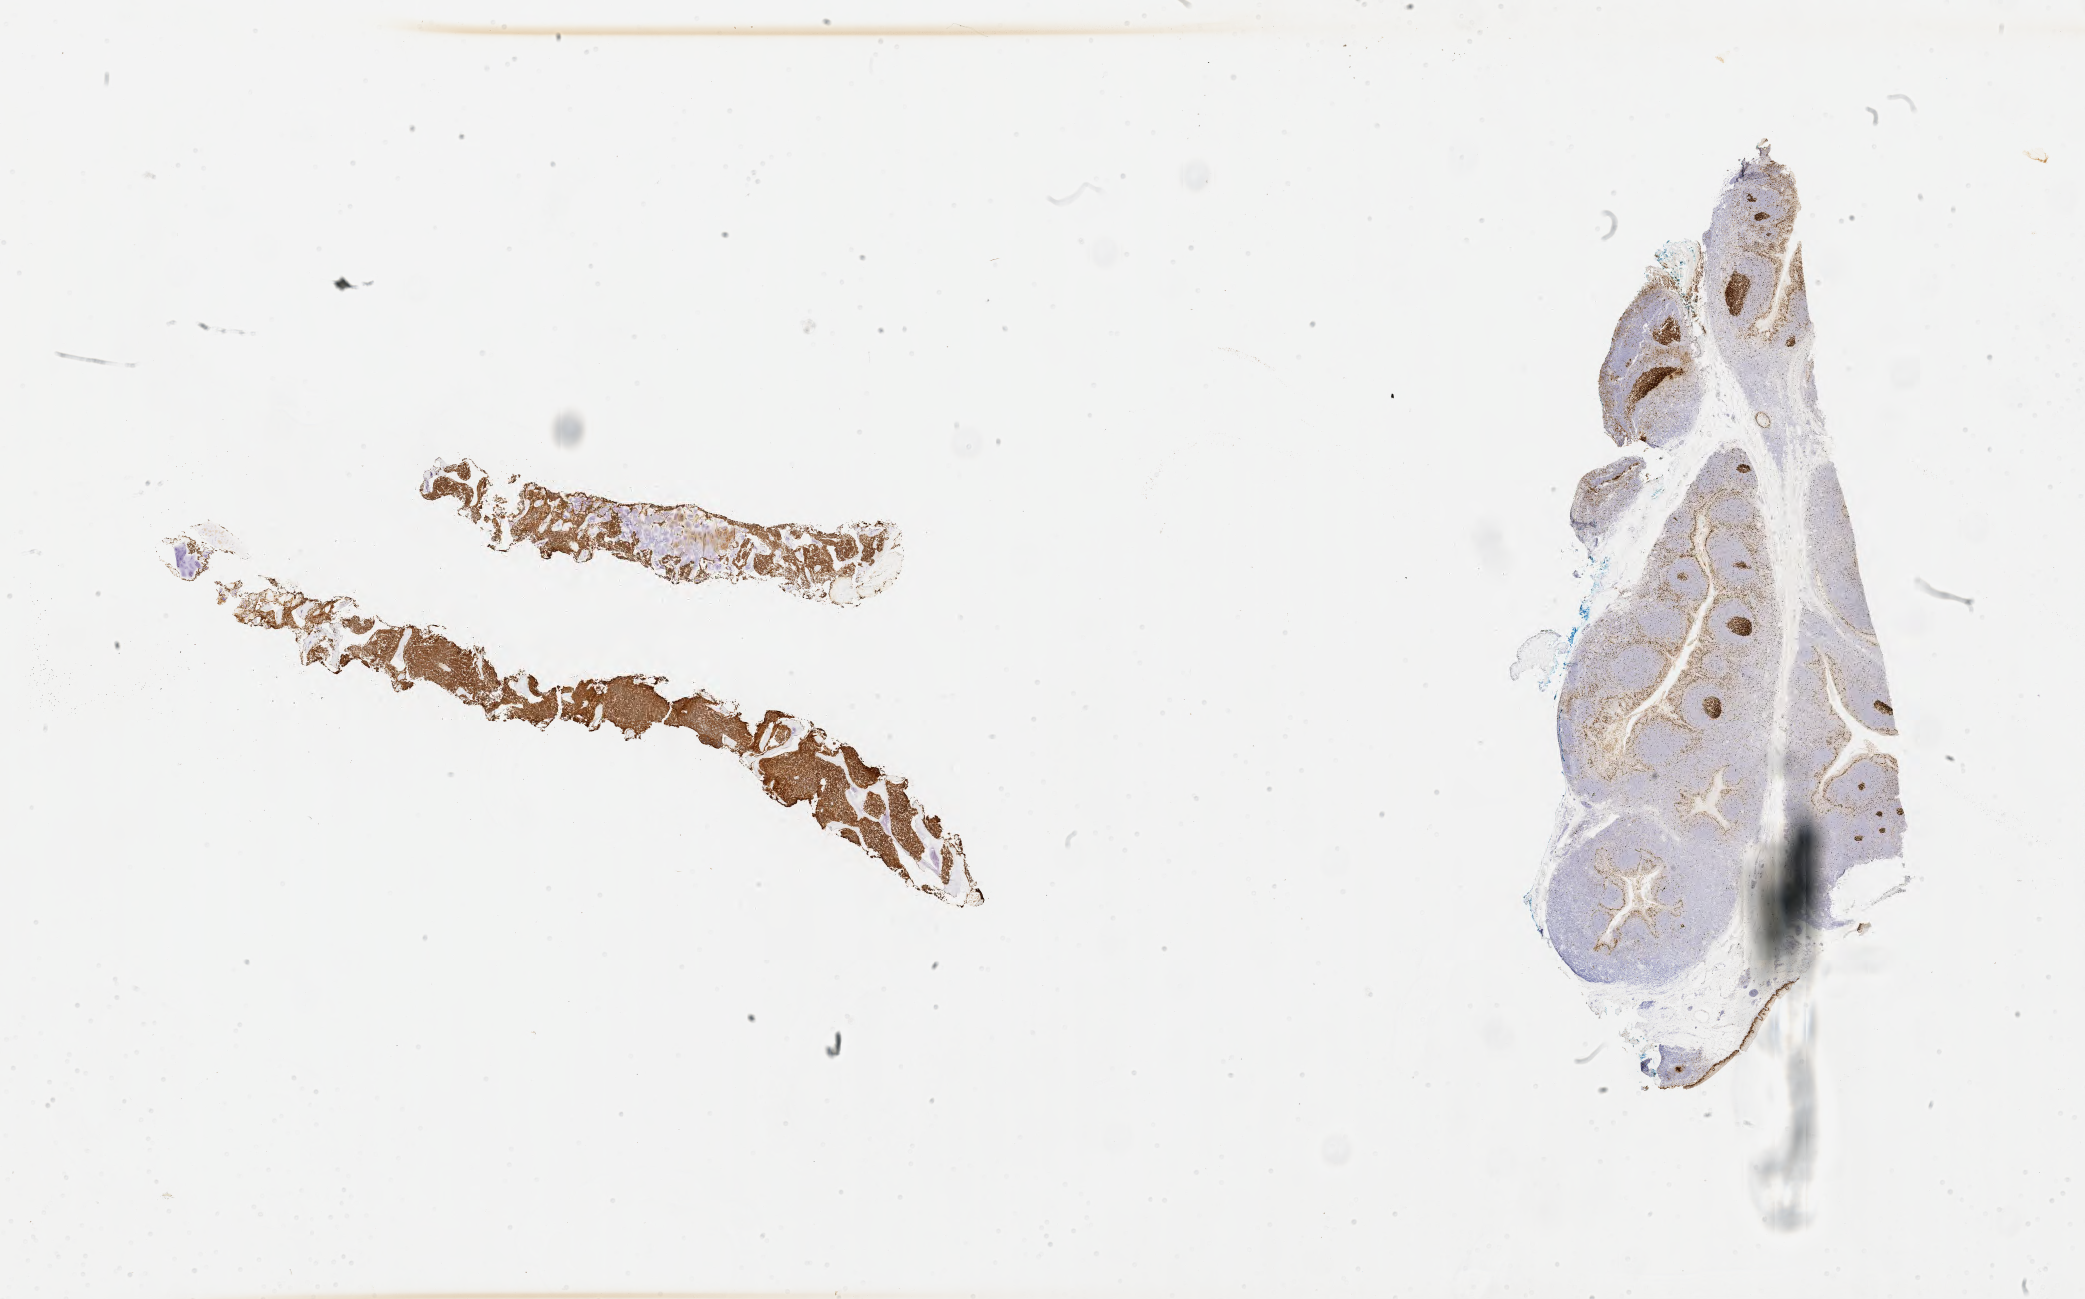
Whole-slide image, immunohistochemical stain for Ki-67 — low-resolution overview of the scanned area, about 33.7 x 21.0 mm; specimen: tumor tissue; site: bone marrow. Patient: male, 11 years old.
Histologic diagnosis: Burkitt lymphoma, NOS.